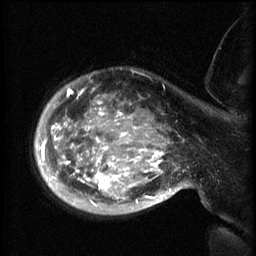
Breast MRI (dynamic contrast-enhanced), one sagittal slice. Position 48 of 60 along the scan axis. 3 images stored at this slice position (order not interpretable as contrast timing). 1.5 T. TE 4.2 ms, TR 8.2 ms. 2.3 mm slice thickness. 256 × 256 image matrix, field of view 200 × 200 mm. Female patient, age 50 years.
Outlined on this slice (semi-automatic segmentation, software-assisted and operator-edited):
- analysis volume of interest (the breast-tissue region the enhancement analysis was run in; not a lesion): bounding box [x1, y1, x2, y2] px = [50, 76, 169, 215]
- tumour enhancement mask (voxels above the 70 % enhancement threshold inside the analysis volume of interest): [52, 88, 167, 207]